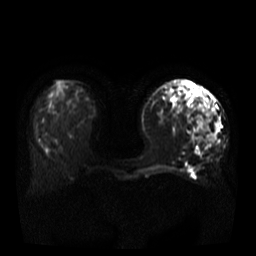
Breast MRI, one axial slice. Position 13 of 37 along the scan axis. Diffusion-weighted series; image 2 of 4 stored at this slice position (different b-values; order by instance number). 3 T. 5 mm slice thickness. 256 × 256 image matrix, field of view 380 × 380 mm. Female patient.
Structures marked on this image (expert manual segmentation):
- tumour on diffusion-weighted imaging: box from (x=195, y=96) to (x=220, y=143) px